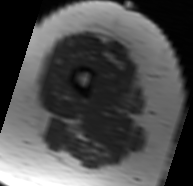
MRI of an extremity soft-tissue mass, one axial slice. Slice 12 of 91 in the series (ordered by position). MR volume resampled by the dataset authors to the PET/CT grid (not the native acquisition matrix). 3.27 mm slice thickness. 193 × 186 image matrix, field of view 188 × 182 mm. Female patient. From the clinical record (not read from this slice): histological type: malignant solitary fibrous tumor; grade: intermediate; site of the primary tumour: right thigh.
Outlined on this slice (expert contour drawn on MRI and transferred to this co-registered scan by the dataset authors):
- gross tumour volume including surrounding oedema: bounding box [x1, y1, x2, y2] px = [77, 39, 125, 70]